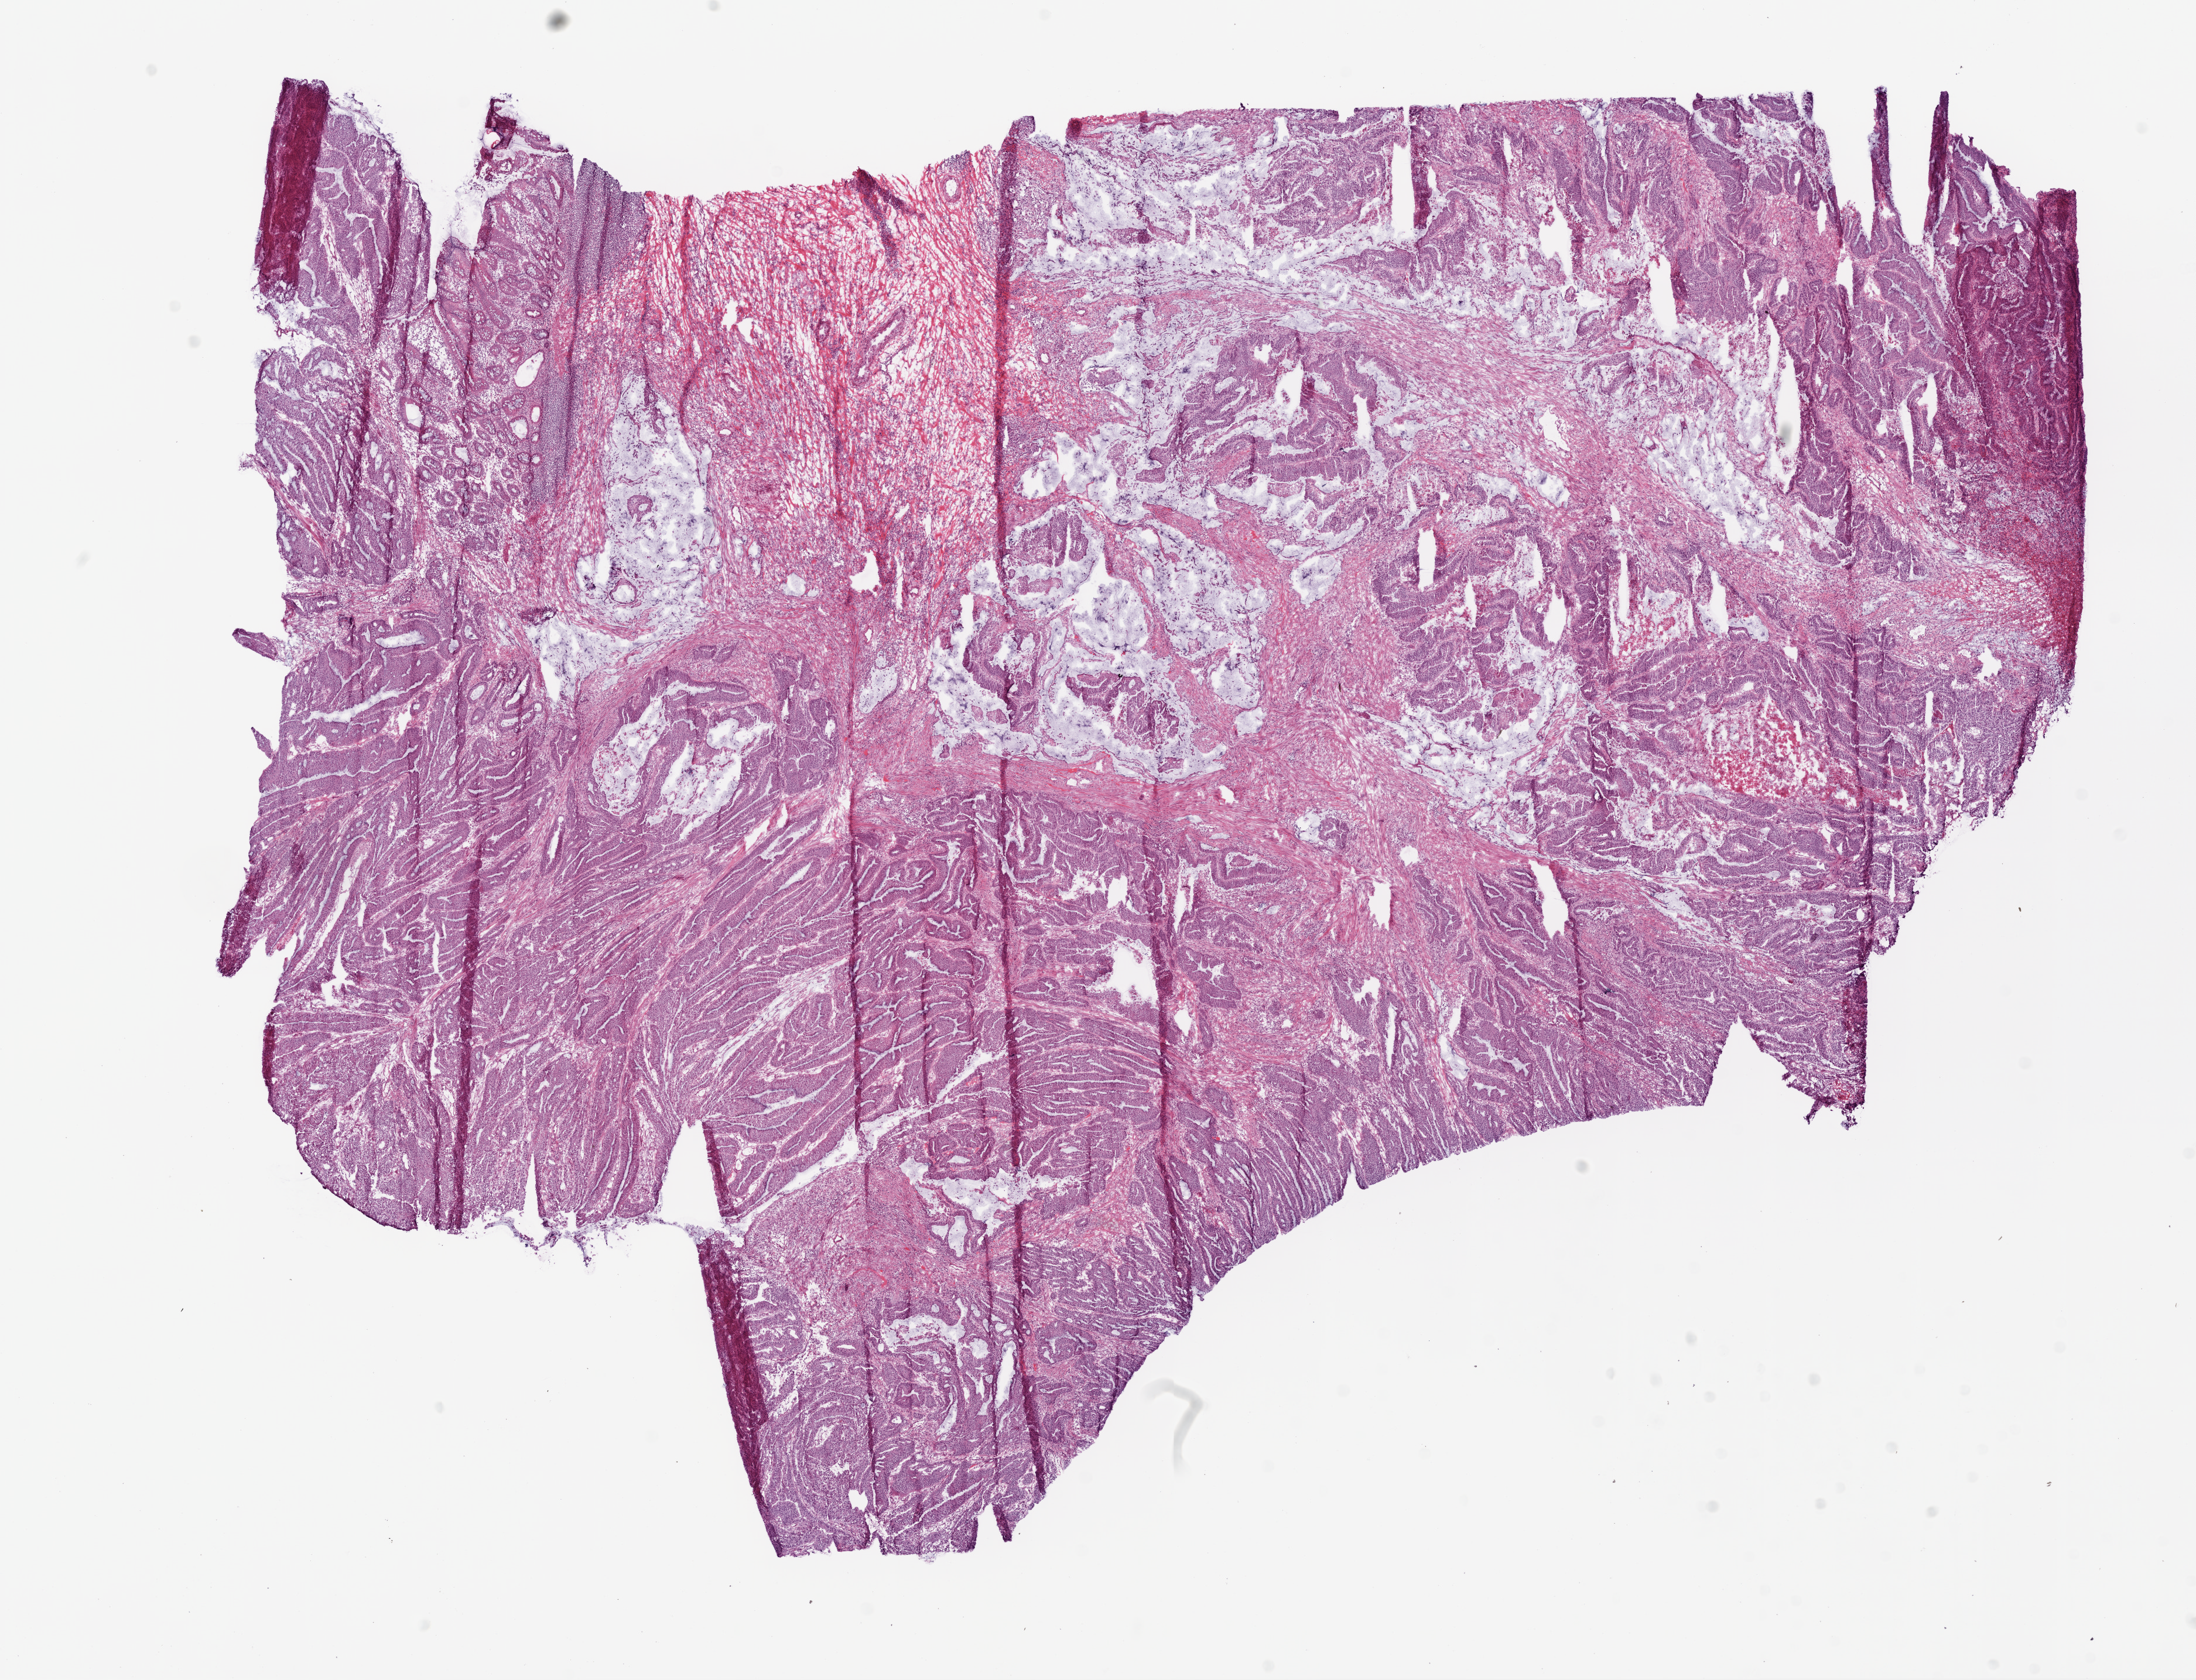
Digitized H&E-stained tissue section (whole slide) — shown as a low-resolution overview of the whole scanned area (about 15.0 x 11.5 mm, slide scanned at 20x); frozen section; sample: primary tumour, colon. Male patient; age at initial diagnosis 71 years.
Diagnosis: Adenocarcinoma, NOS (cecum).